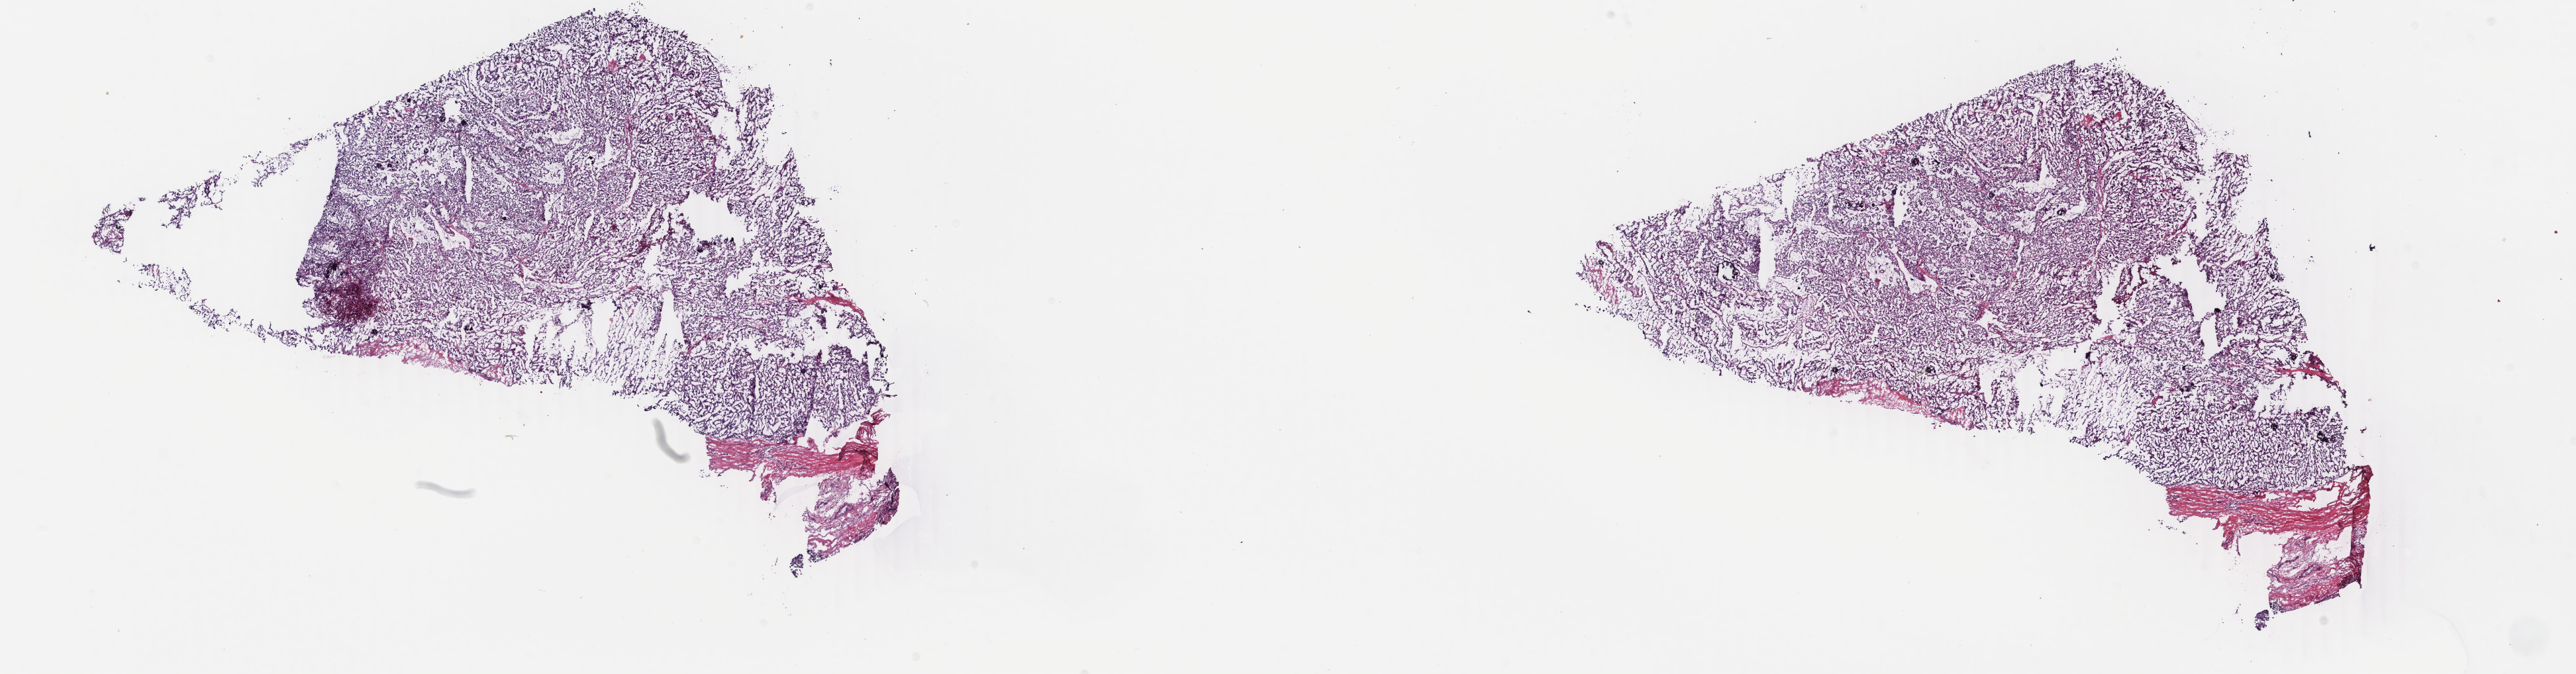
H&E whole-slide image, whole scanned area (about 30.9 x 8.1 mm, slide scanned at 40x) shown as a low-resolution overview, frozen section from the top of the tissue portion, sample: primary tumour, thyroid. Female, age 30 years at initial diagnosis. Slide review estimates, as recorded: tumour cells 90%, tumour nuclei 90%, normal cells 0%, stromal cells 10%, necrosis 0%. Inflammatory infiltration, as recorded: lymphocyte infiltration 1%, monocyte infiltration 0%, neutrophil infiltration 0%.
Pathologic diagnosis: Papillary adenocarcinoma, NOS. AJCC pathologic stage: I. TNM: T3 N1 M0. Lymph nodes positive (case pathology): 2 of 2 examined.